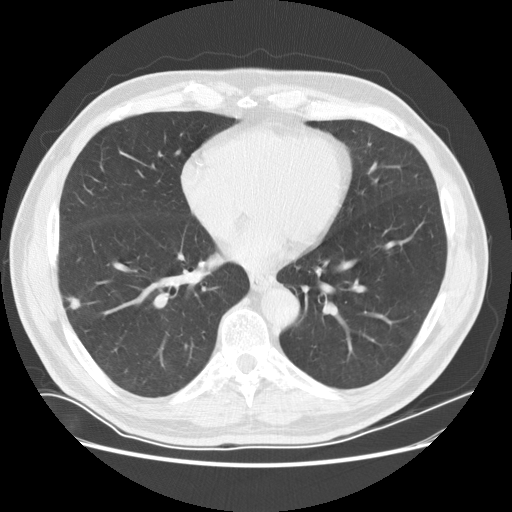
Axial slice from a low-dose chest CT screening exam, baseline screening round, lung window (W 1500 / L -600 HU), 2.5 mm slice thickness, standard (soft-tissue) reconstruction kernel (STANDARD), 512 × 512 image matrix, field of view 380 × 380 mm. Male, age 72 years at enrolment. Current smoker at enrolment.
Expert-annotated lung lesion, box from (x=55, y=291) to (x=91, y=323) px. Reader record for this screening exam (exam-level; its link to the box is not recorded): non-calcified nodule or mass ≥4 mm, right lower lobe, 13 × 8 mm, poorly defined margins, soft tissue attenuation. Lung cancer was diagnosed 17 days after this screen: non-small cell carcinoma, right lower lobe, moderately differentiated (G2), stage IA (AJCC 6th edition), 10 mm at pathology.